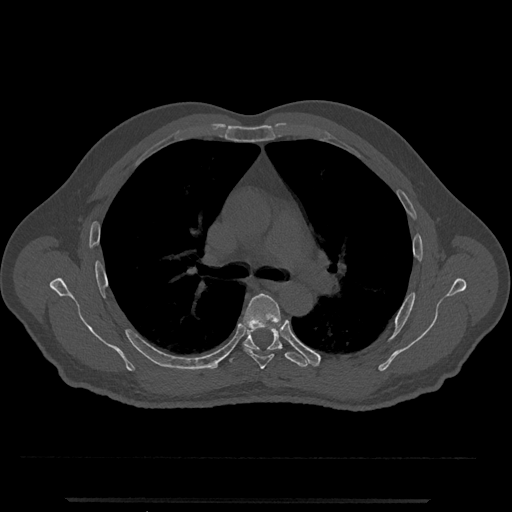
CT including the spine, one axial slice; position 768 of 797 along the scan axis; 120 kVp; bone window (W 1800 / L 400 HU); 0.5 mm slice thickness; 512 × 512 image matrix, field of view 419 × 419 mm. Male patient, age 63 years. Case-level facts recorded for this patient, not image findings: primary cancer: prostate.
Outlined on this slice (semi-automatic segmentation, software-assisted and operator-edited):
- T5 vertebra: box from (x=243, y=293) to (x=281, y=369) px
- T6 vertebra: (x=226, y=322)–(x=308, y=367)